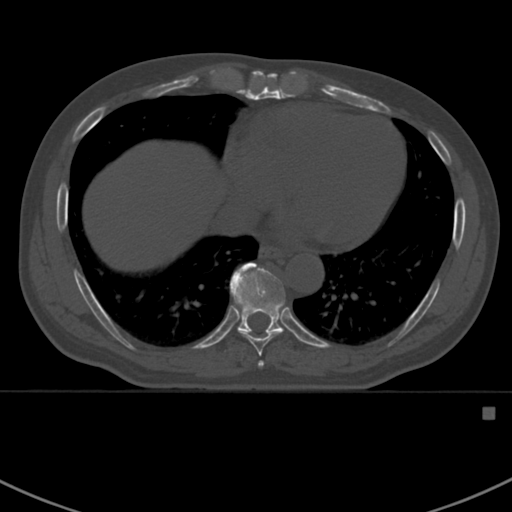
CT including the spine, one axial slice; slice 392 of 412 in the series (ordered by position); reconstruction kernel Br40s; 120 kVp; bone window (W 1800 / L 400 HU); 1.5 mm slice thickness; 512 × 512 image matrix, field of view 358 × 358 mm. Male patient, age 59 years. Case-level facts recorded for this patient, not image findings: primary cancer: prostate.
Structures marked on this image (semi-automatically segmented with operator editing):
- T7 vertebra: bounding box [x1, y1, x2, y2] px = [258, 361, 264, 367]
- T8 vertebra: [242, 332, 282, 357]
- T9 vertebra: [230, 262, 297, 338]